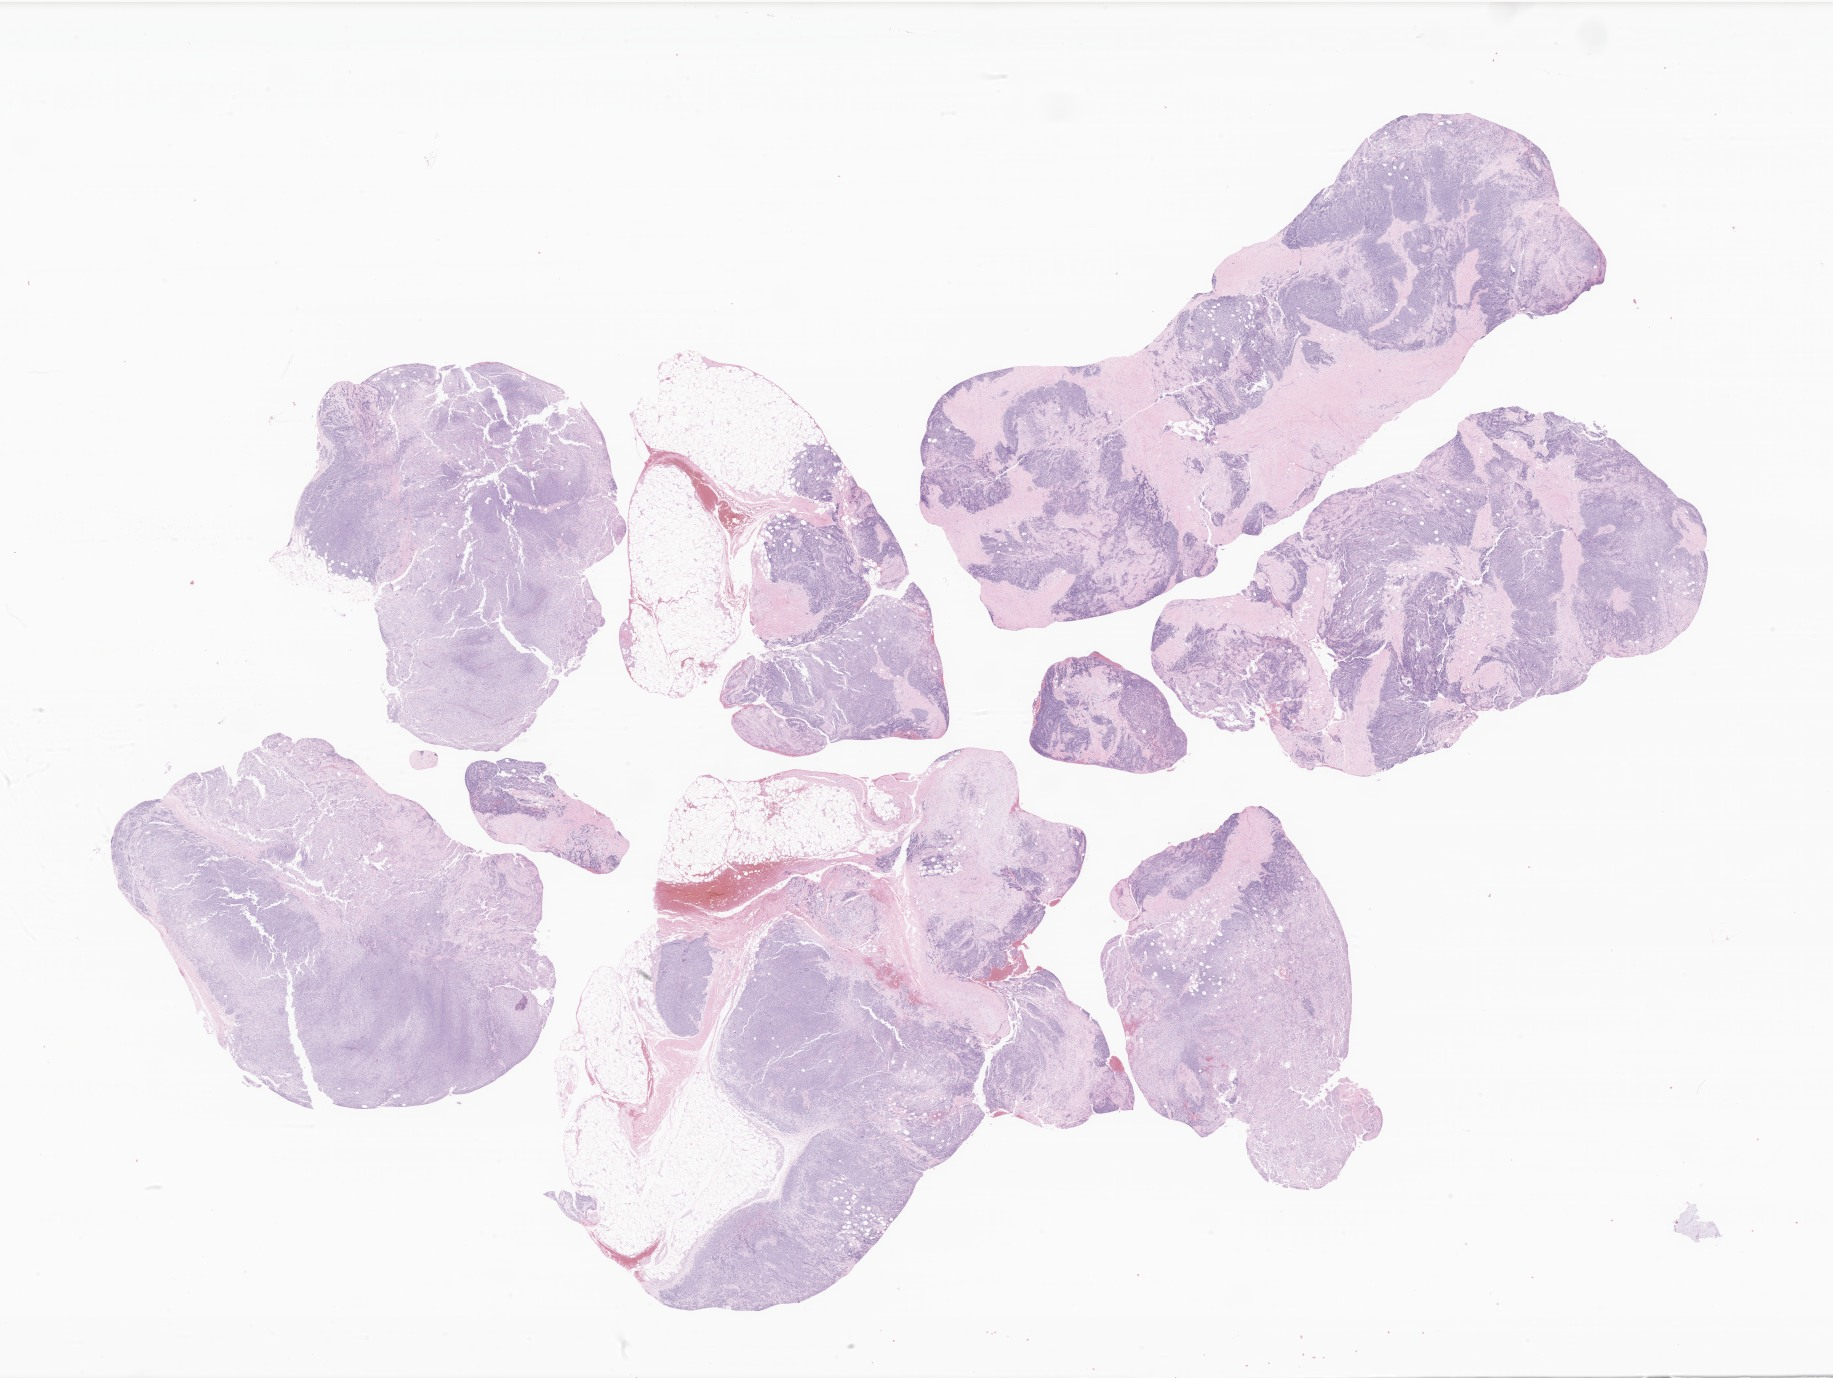
Whole-slide image, H&E stain of tumor tissue from the soft tissue of pelvis, a low-resolution overview of the entire scanned area, about 30.9 x 23.2 mm; FFPE section. Patient: female, age 122 months (10 years 2 months).
Diagnosis: Rhabdomyosarcoma, NOS.